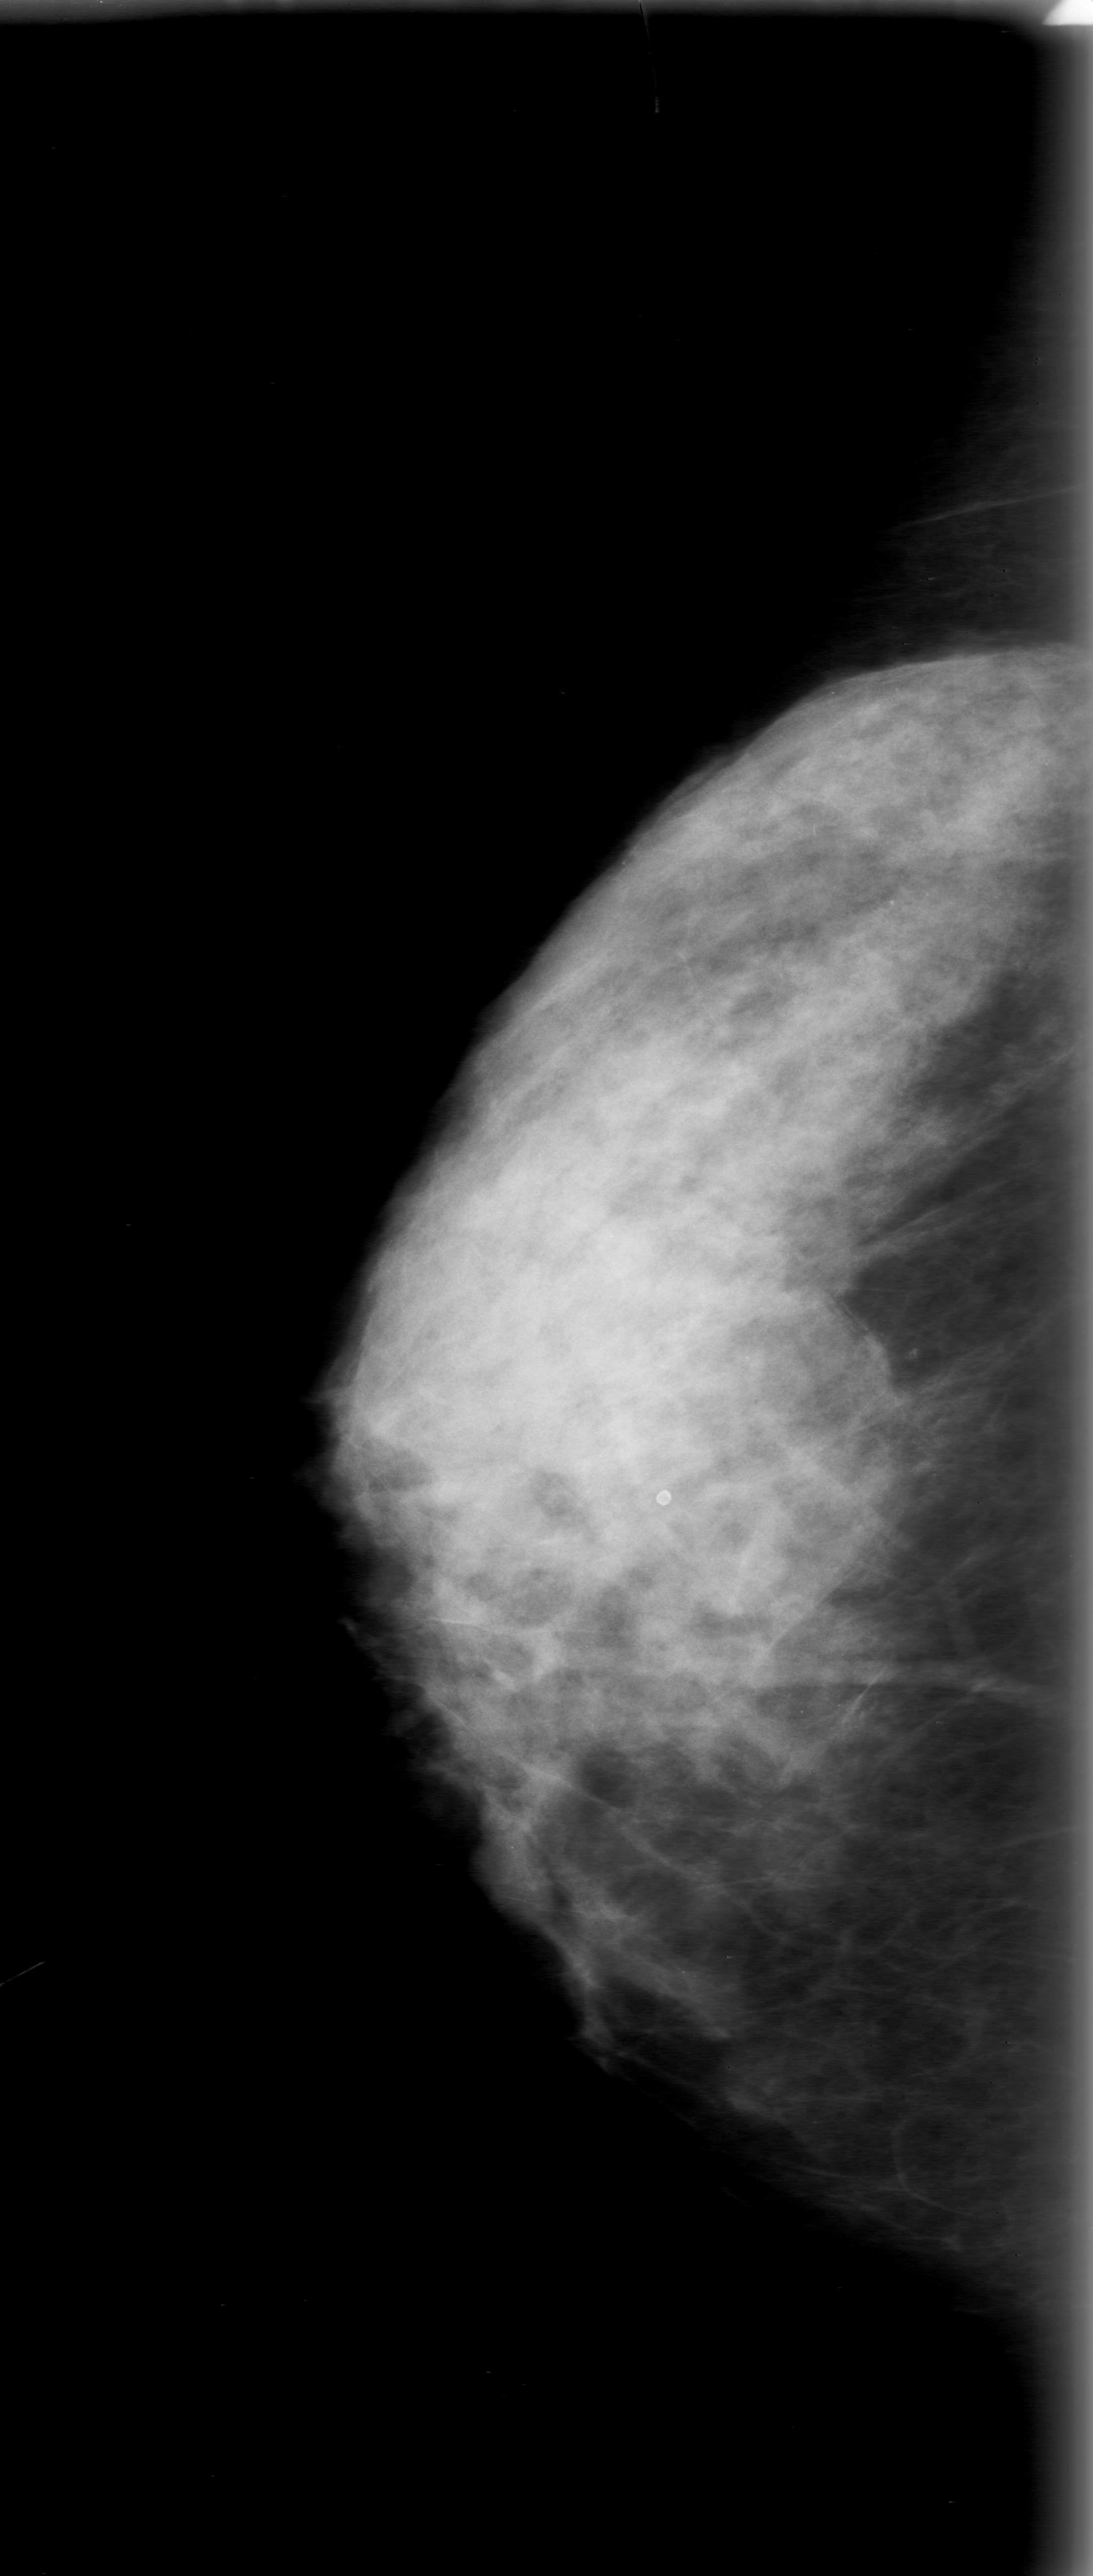
Scanned film-screen mammogram; right breast; CC view; BI-RADS breast density category 4 (scale 1–4).
Marked abnormality: mass, shape lobulated, margins obscured; BI-RADS assessment category 0 (incomplete: needs additional imaging); subtlety rating 3 on a 1 (subtle) to 5 (obvious) scale; pathology (as recorded): benign.